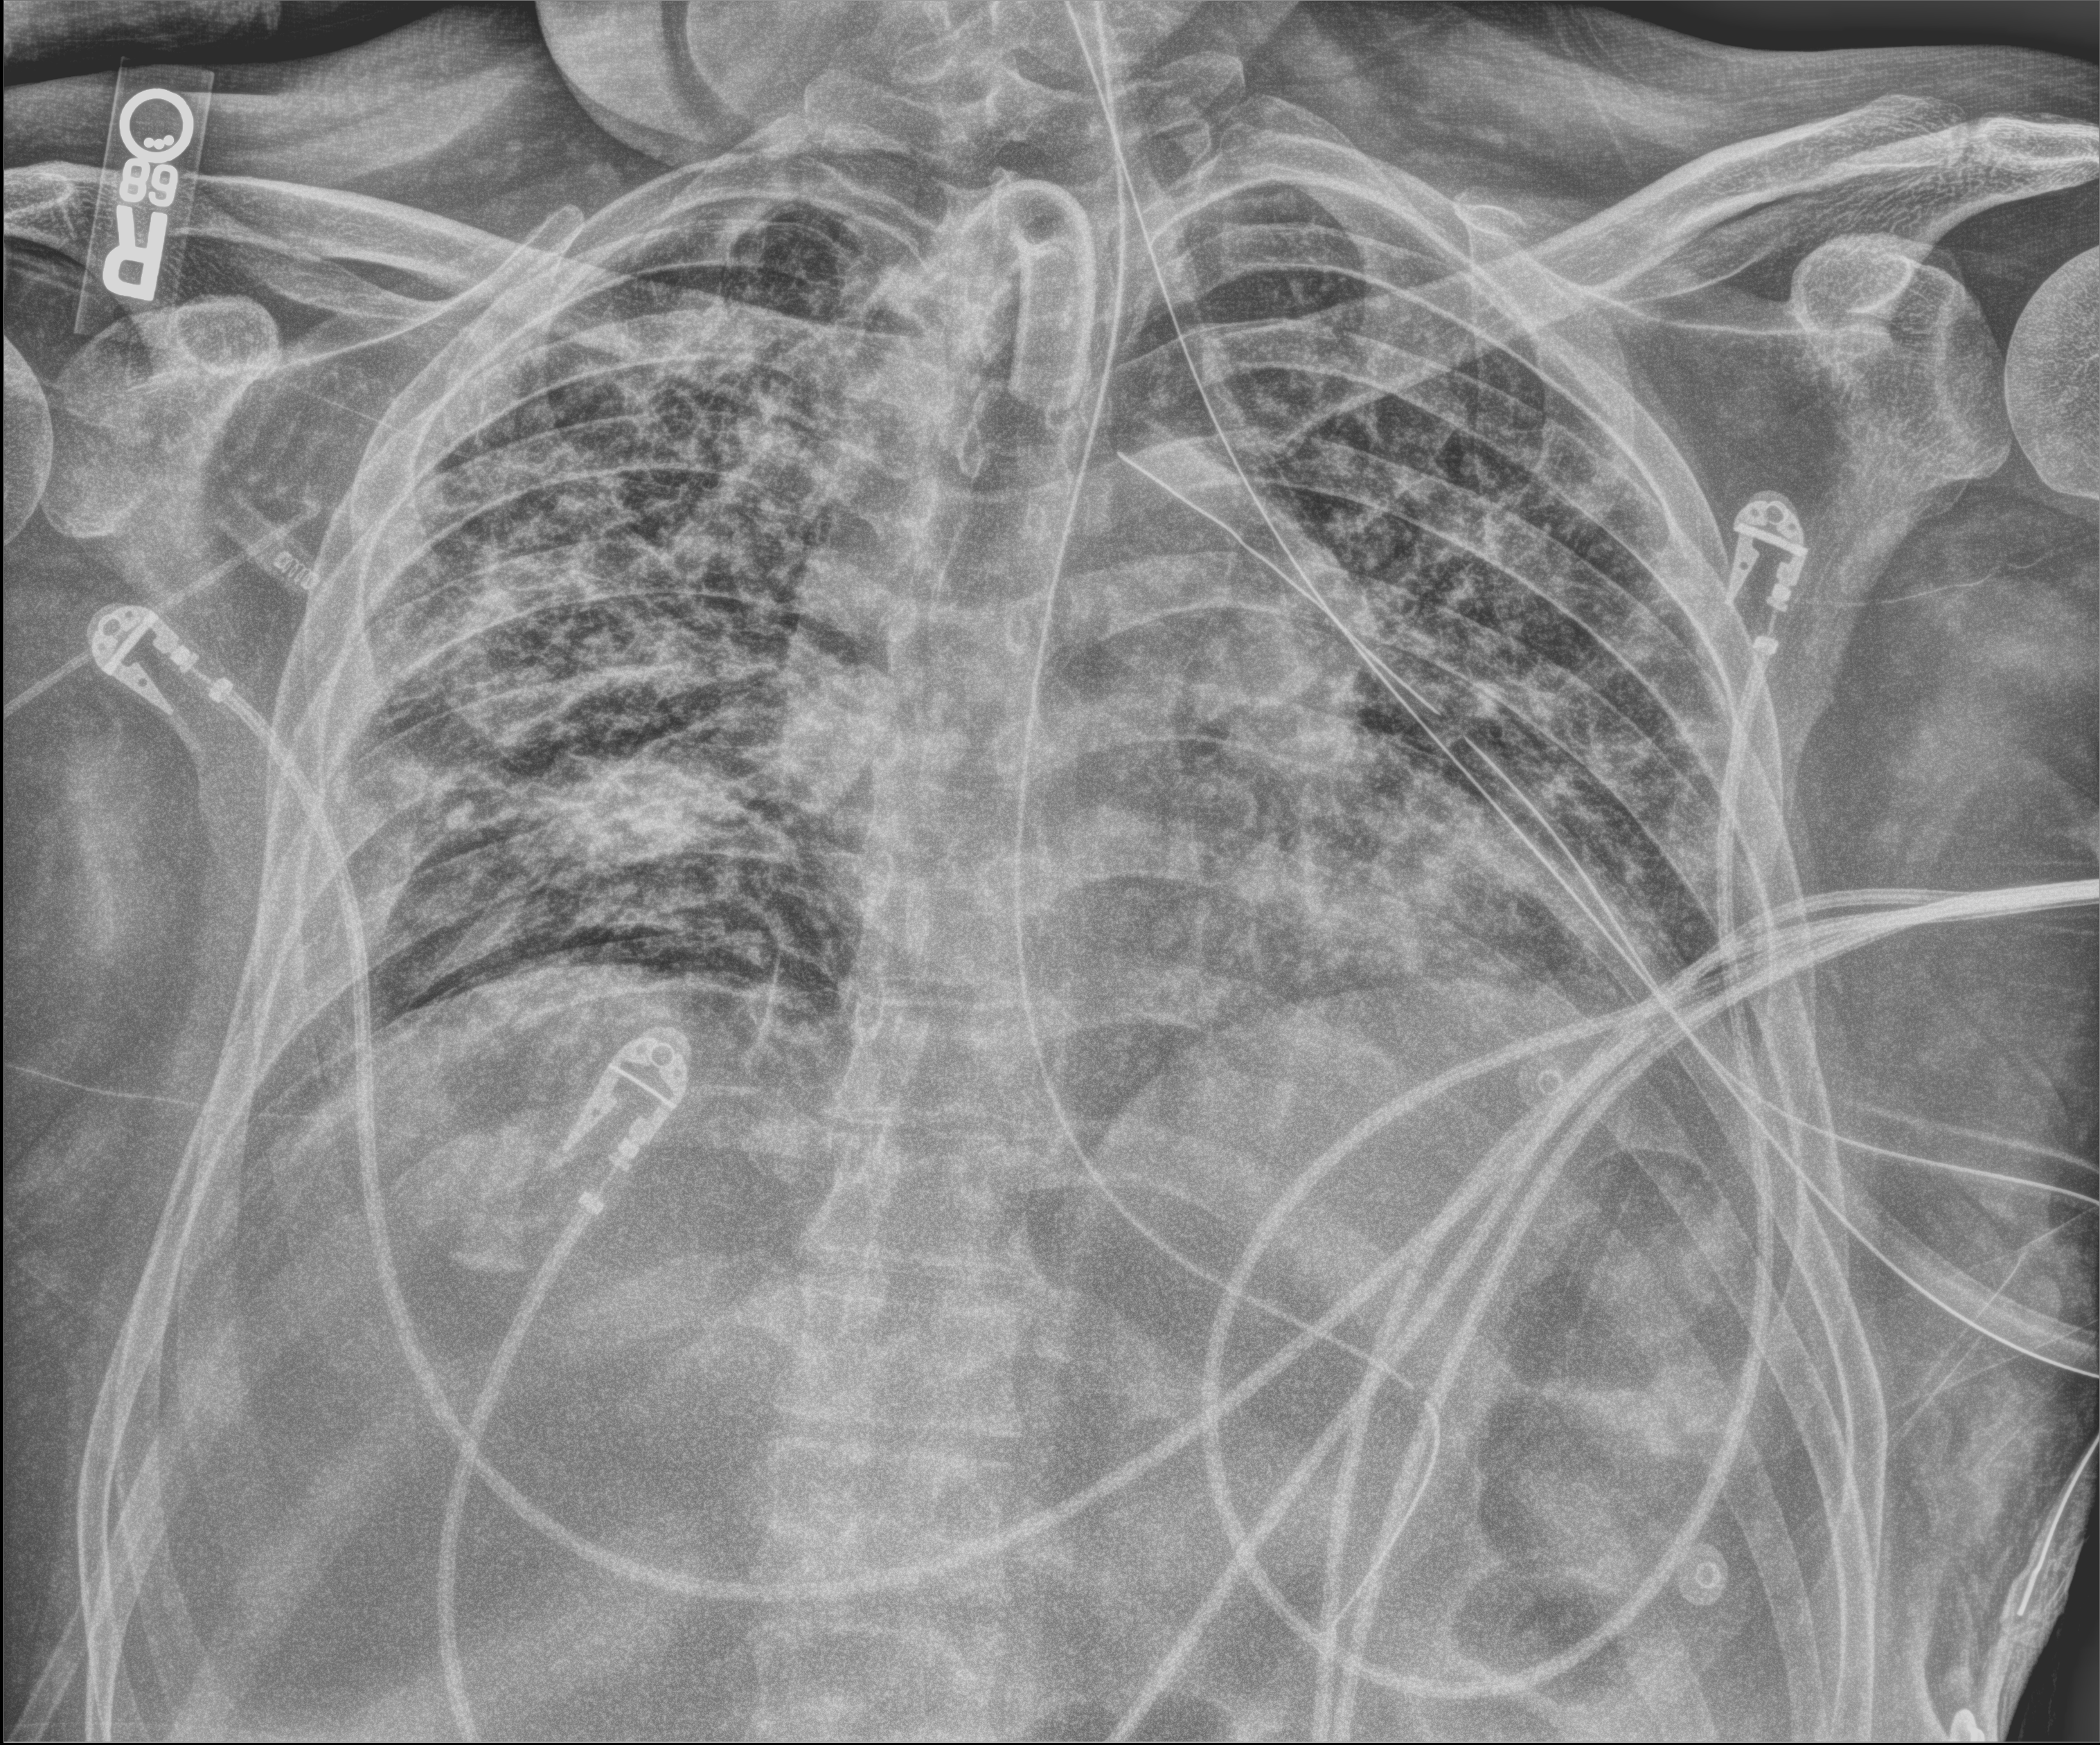
Chest radiograph, anteroposterior (AP) projection. Male patient hospitalised with COVID-19, age 18–59 years.
Hospital-stay facts (about this admission, not read from this image; timing relative to this image not recorded):
- mechanically ventilated during this hospital stay: yes